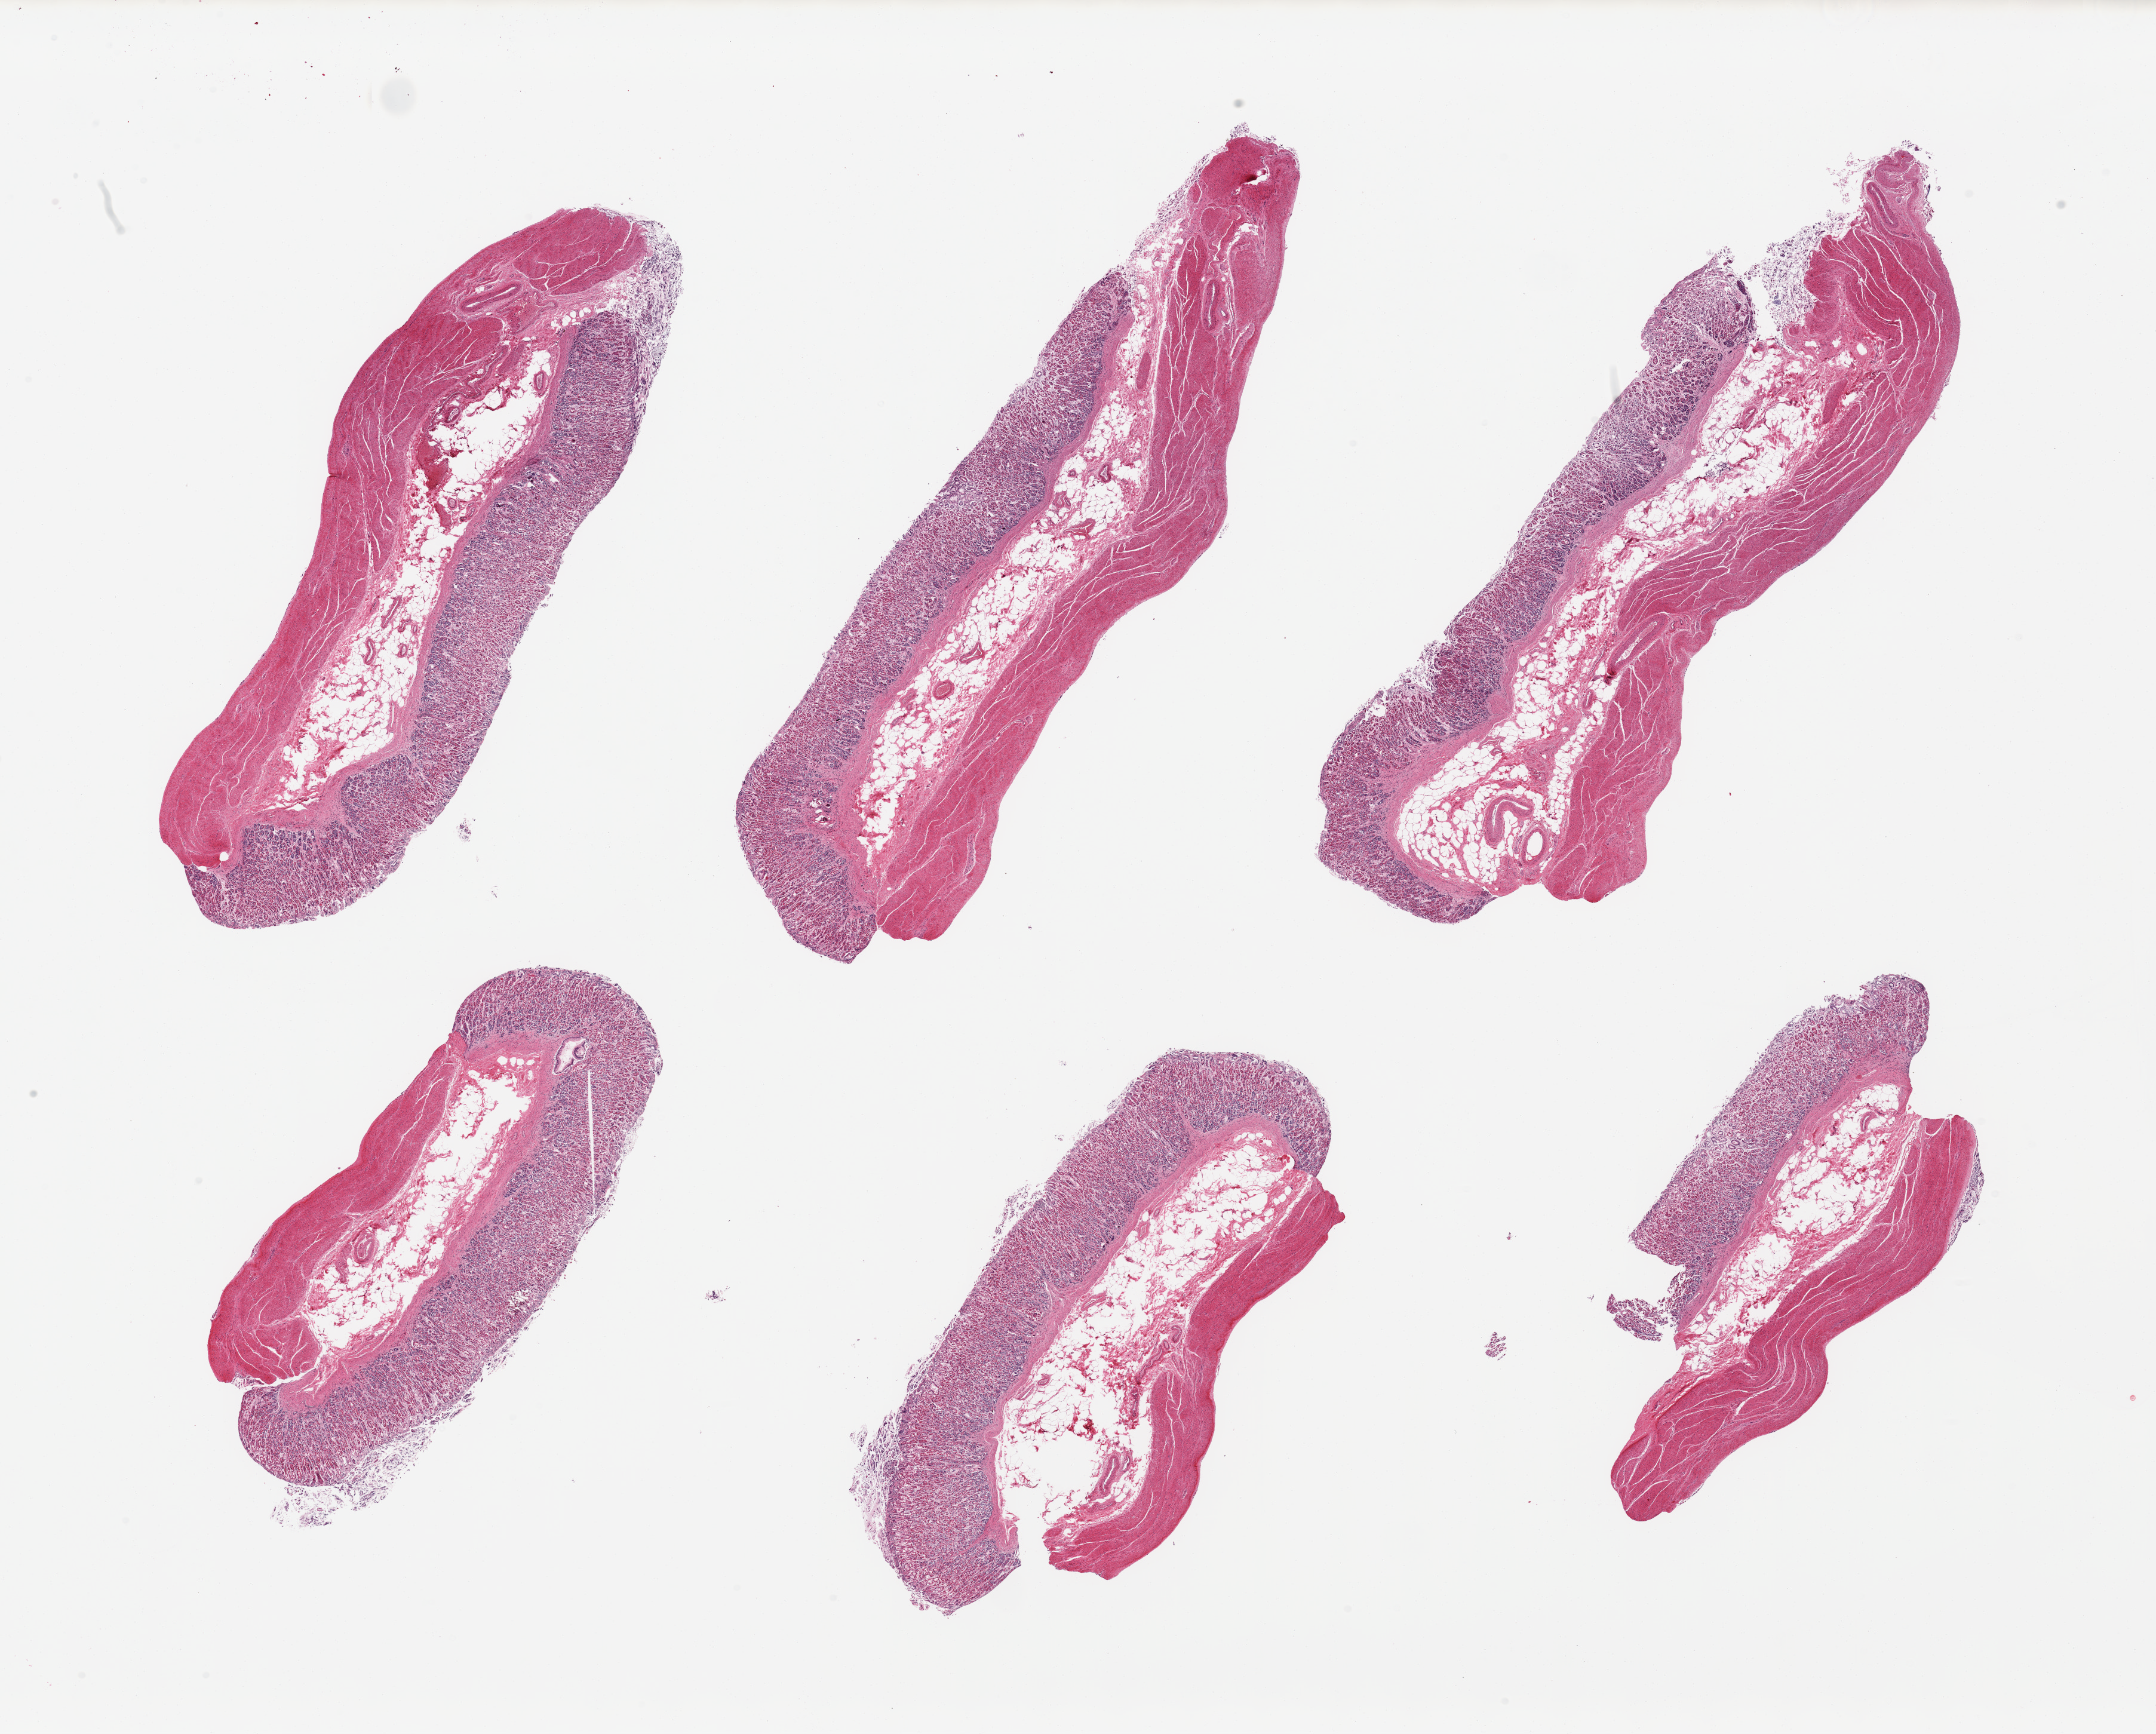
H&E whole-slide image, brightfield — a low-resolution overview of the entire scanned area, about 28.5 x 23.0 mm (acquisition: 20x scan). PAXgene-fixed paraffin-embedded (PFPE) section. Section of stomach (target tissue). Donor tissue sample.
Pathologist's review note for this sample: 6 pieces, mucosa up to ~1.2mm, ~30% thickness, moderately advanced autolysis.